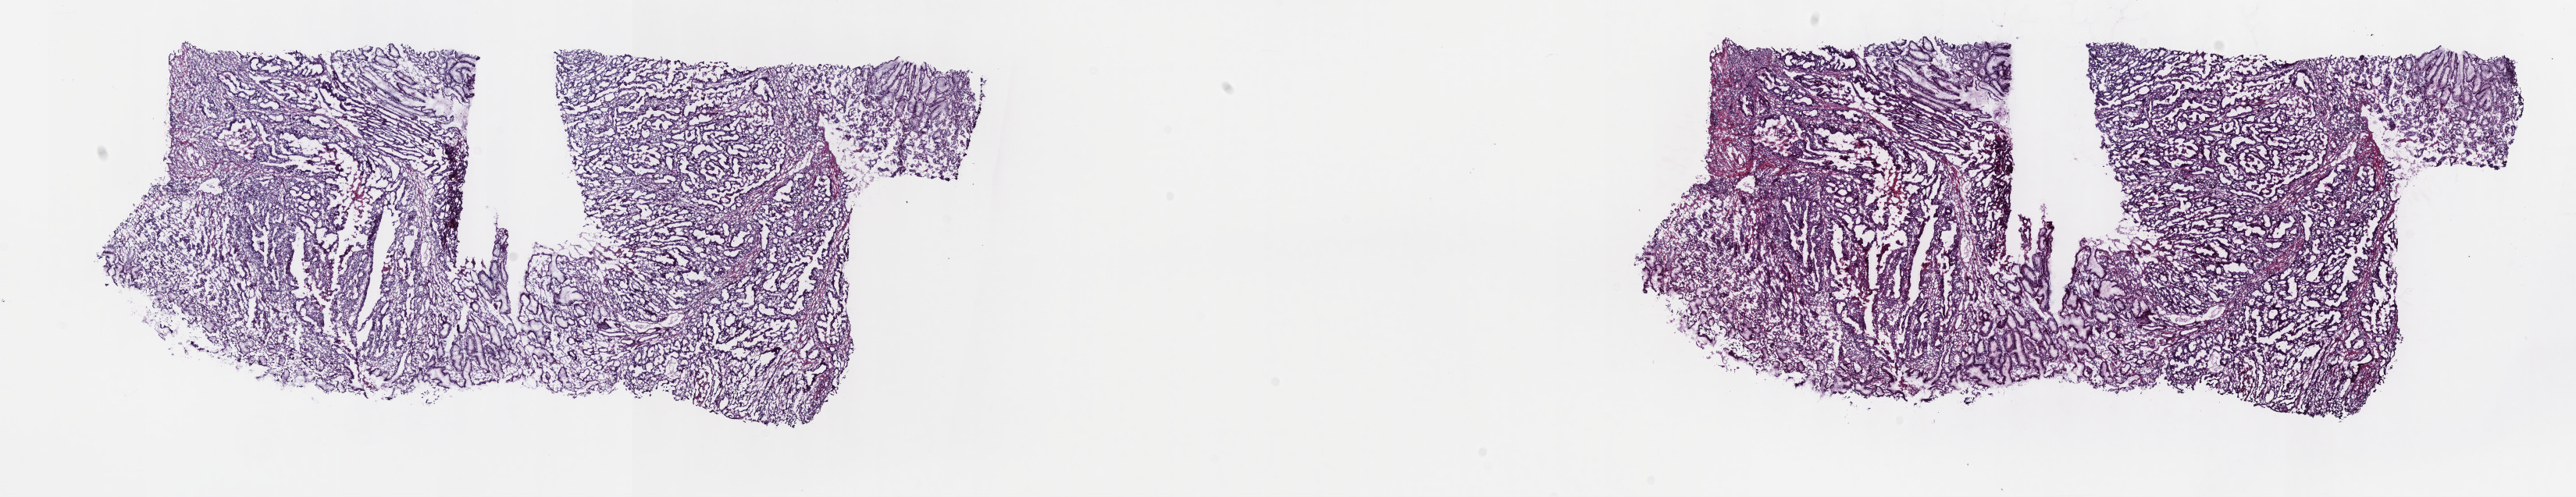
Digitized Hematoxylin and eosin (H&E) stained tissue section (whole slide), low-resolution overview of the scanned area, about 26.7 x 5.2 mm. Frozen section from the top of the tissue portion. Sample: primary tumour, stomach. Male, age 74 years at initial diagnosis. Histologic grade: G3 (poorly differentiated). Pathologist review of this section (percent, as recorded): tumour cells 100%, tumour nuclei 70%, normal cells 0%, stromal cells 0%, necrosis 0%. Infiltration values recorded for this section: lymphocyte infiltration 3%, monocyte infiltration 0%, neutrophil infiltration 0%.
TNM: T3 N2 M0. AJCC pathologic stage: IIIB. Pathologic diagnosis: Adenocarcinoma, intestinal type (gastric antrum).